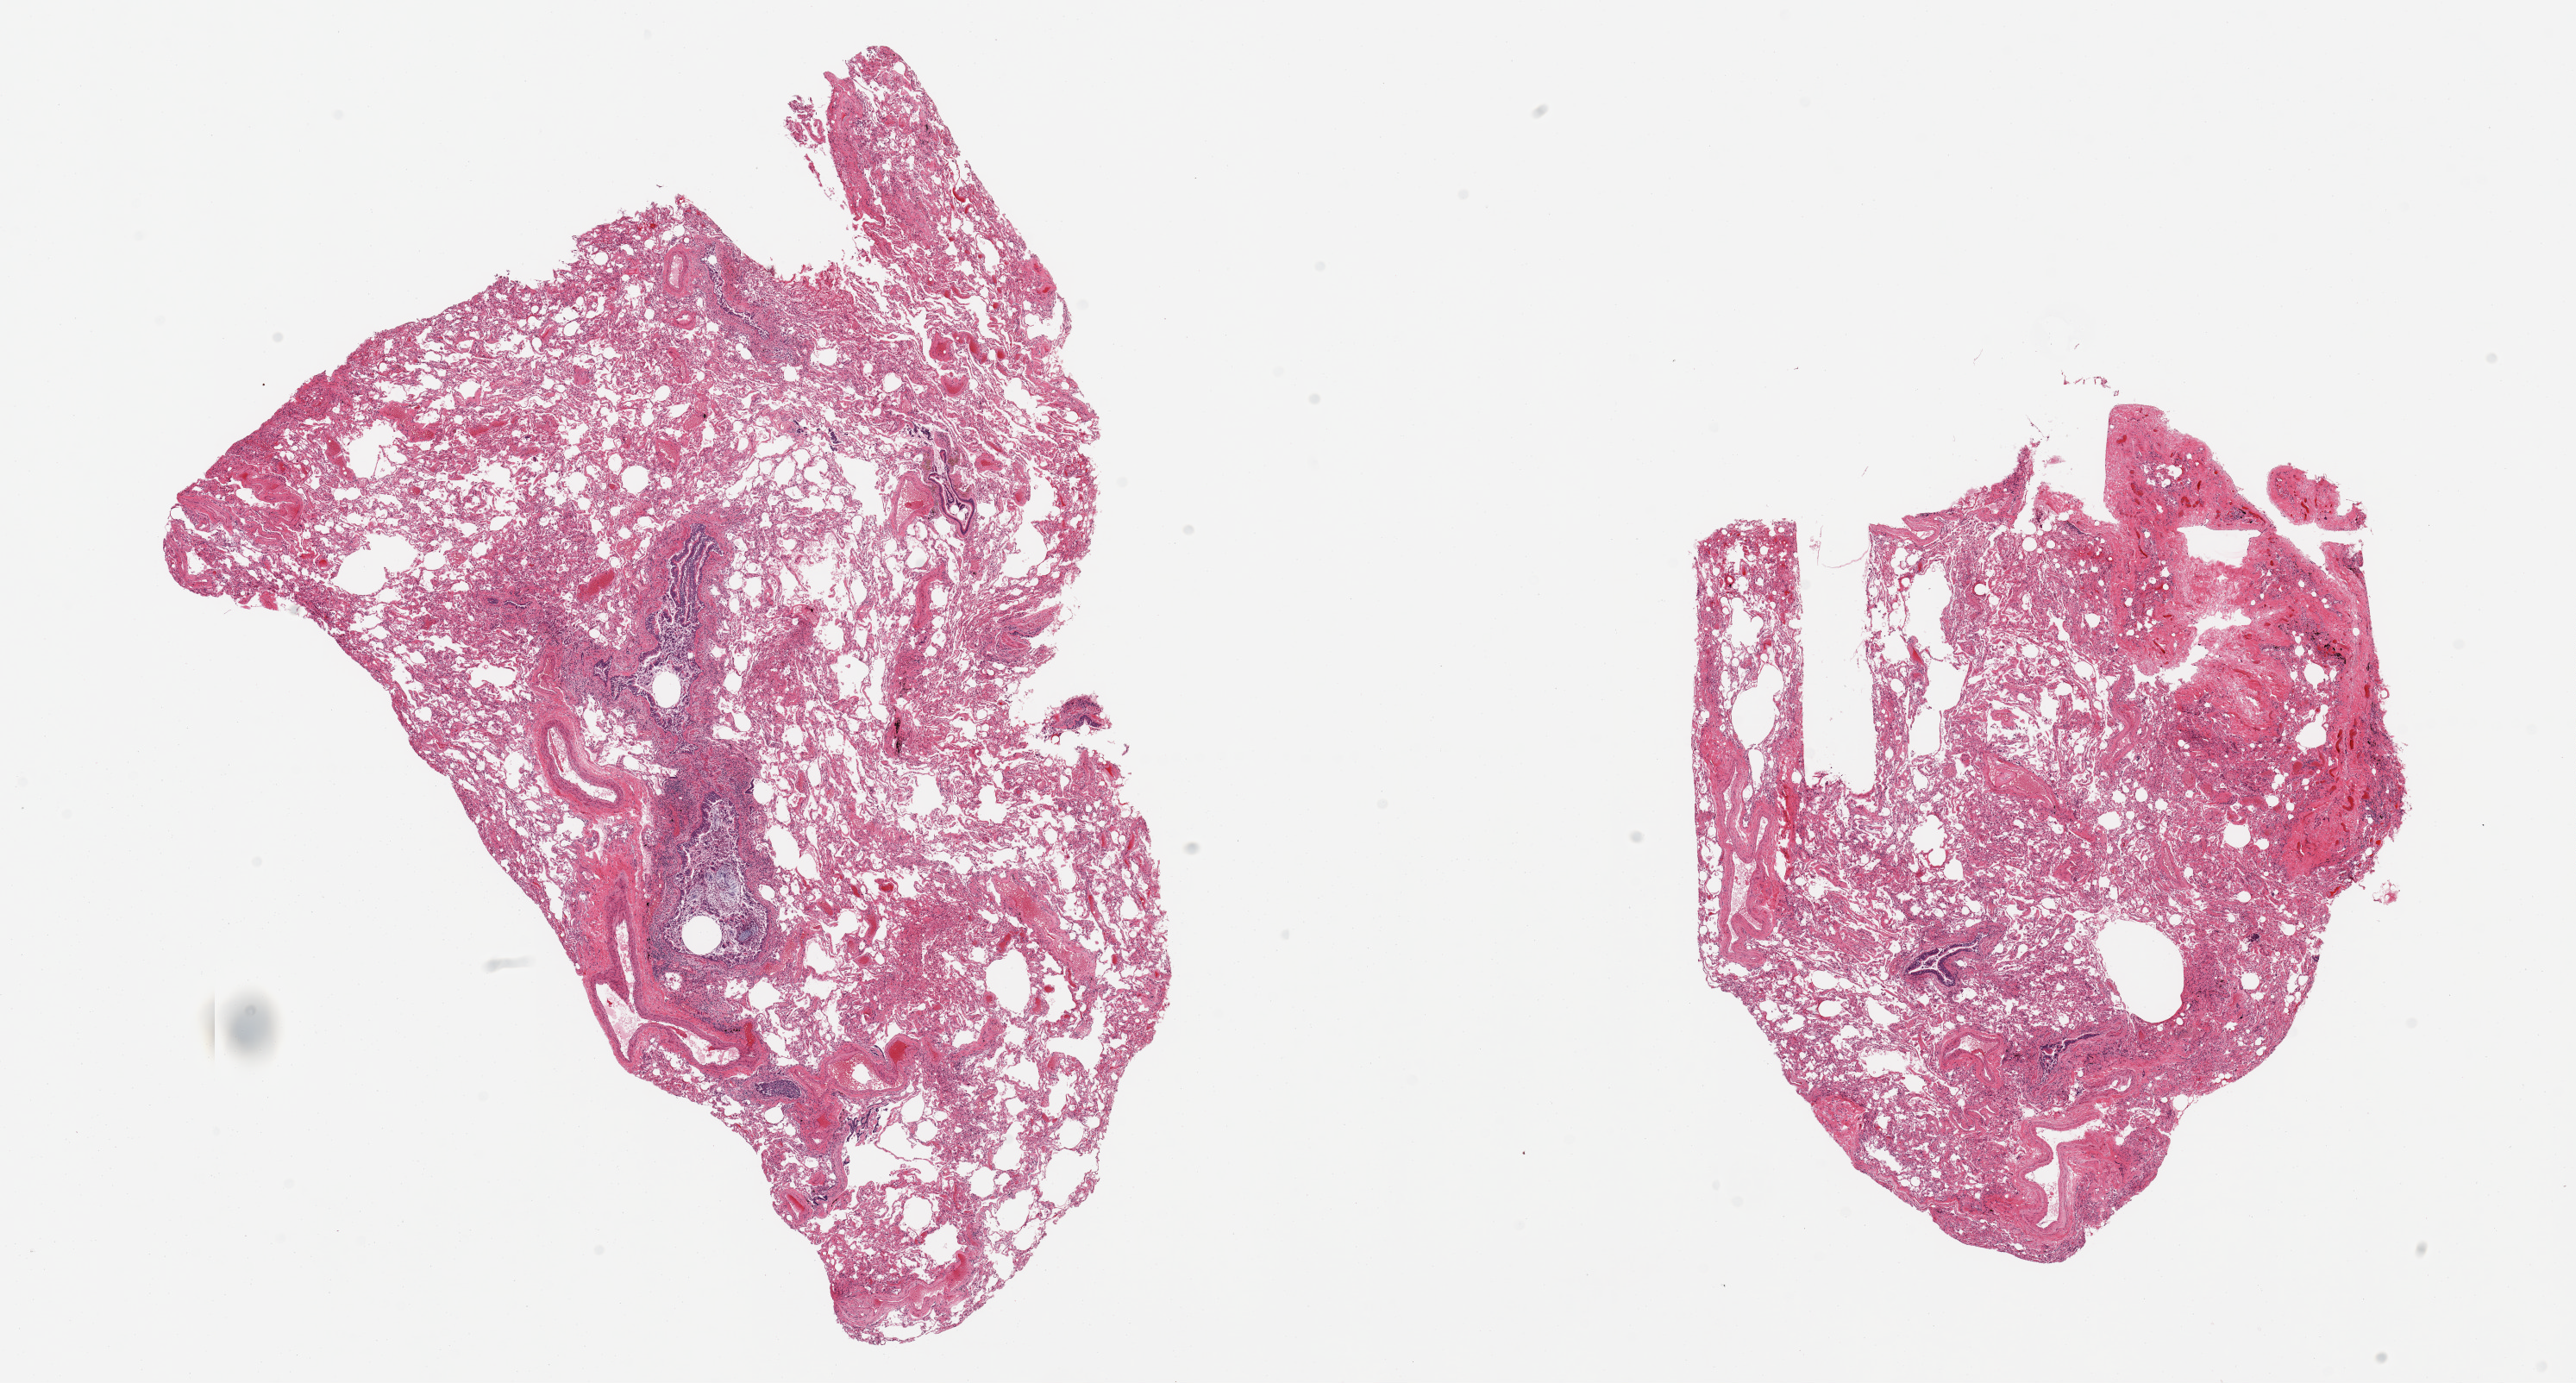
H&E whole-slide image, shown as a low-resolution overview of the whole scanned area (about 23.6 x 12.7 mm, from a 20x scan), PAXgene-fixed, paraffin-embedded tissue, section of lung (target tissue), donor tissue sample. Male donor.
Review note (as recorded): 2 pieces; some congestion and emphysematous change, bronchitis.